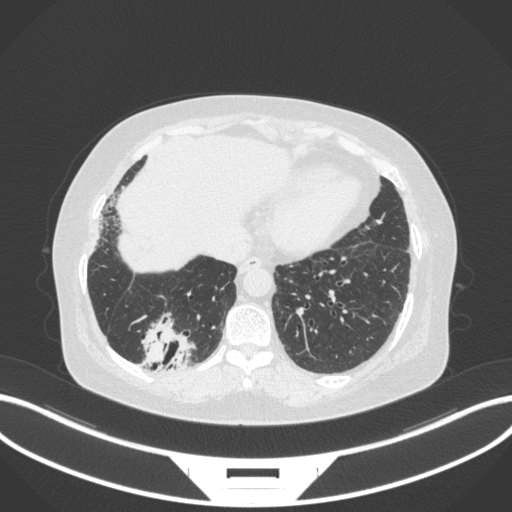
Chest CT, one axial slice; slice 48 of 303 in the series (ordered by position); reconstruction kernel B31f; lung window (W 1500 / L -600 HU); 1 mm slice thickness; 512 × 512 image matrix, field of view 400 × 400 mm. Female patient, age 65 years. From the clinical record (not read from this slice): clinical TNM (as recorded): T2b N1 M0; histopathological grade: G1.
Annotated regions visible in this slice (bounding box drawn by a radiologist):
- lung tumour (recorded histology: adenocarcinoma): box from (x=136, y=310) to (x=198, y=373) px